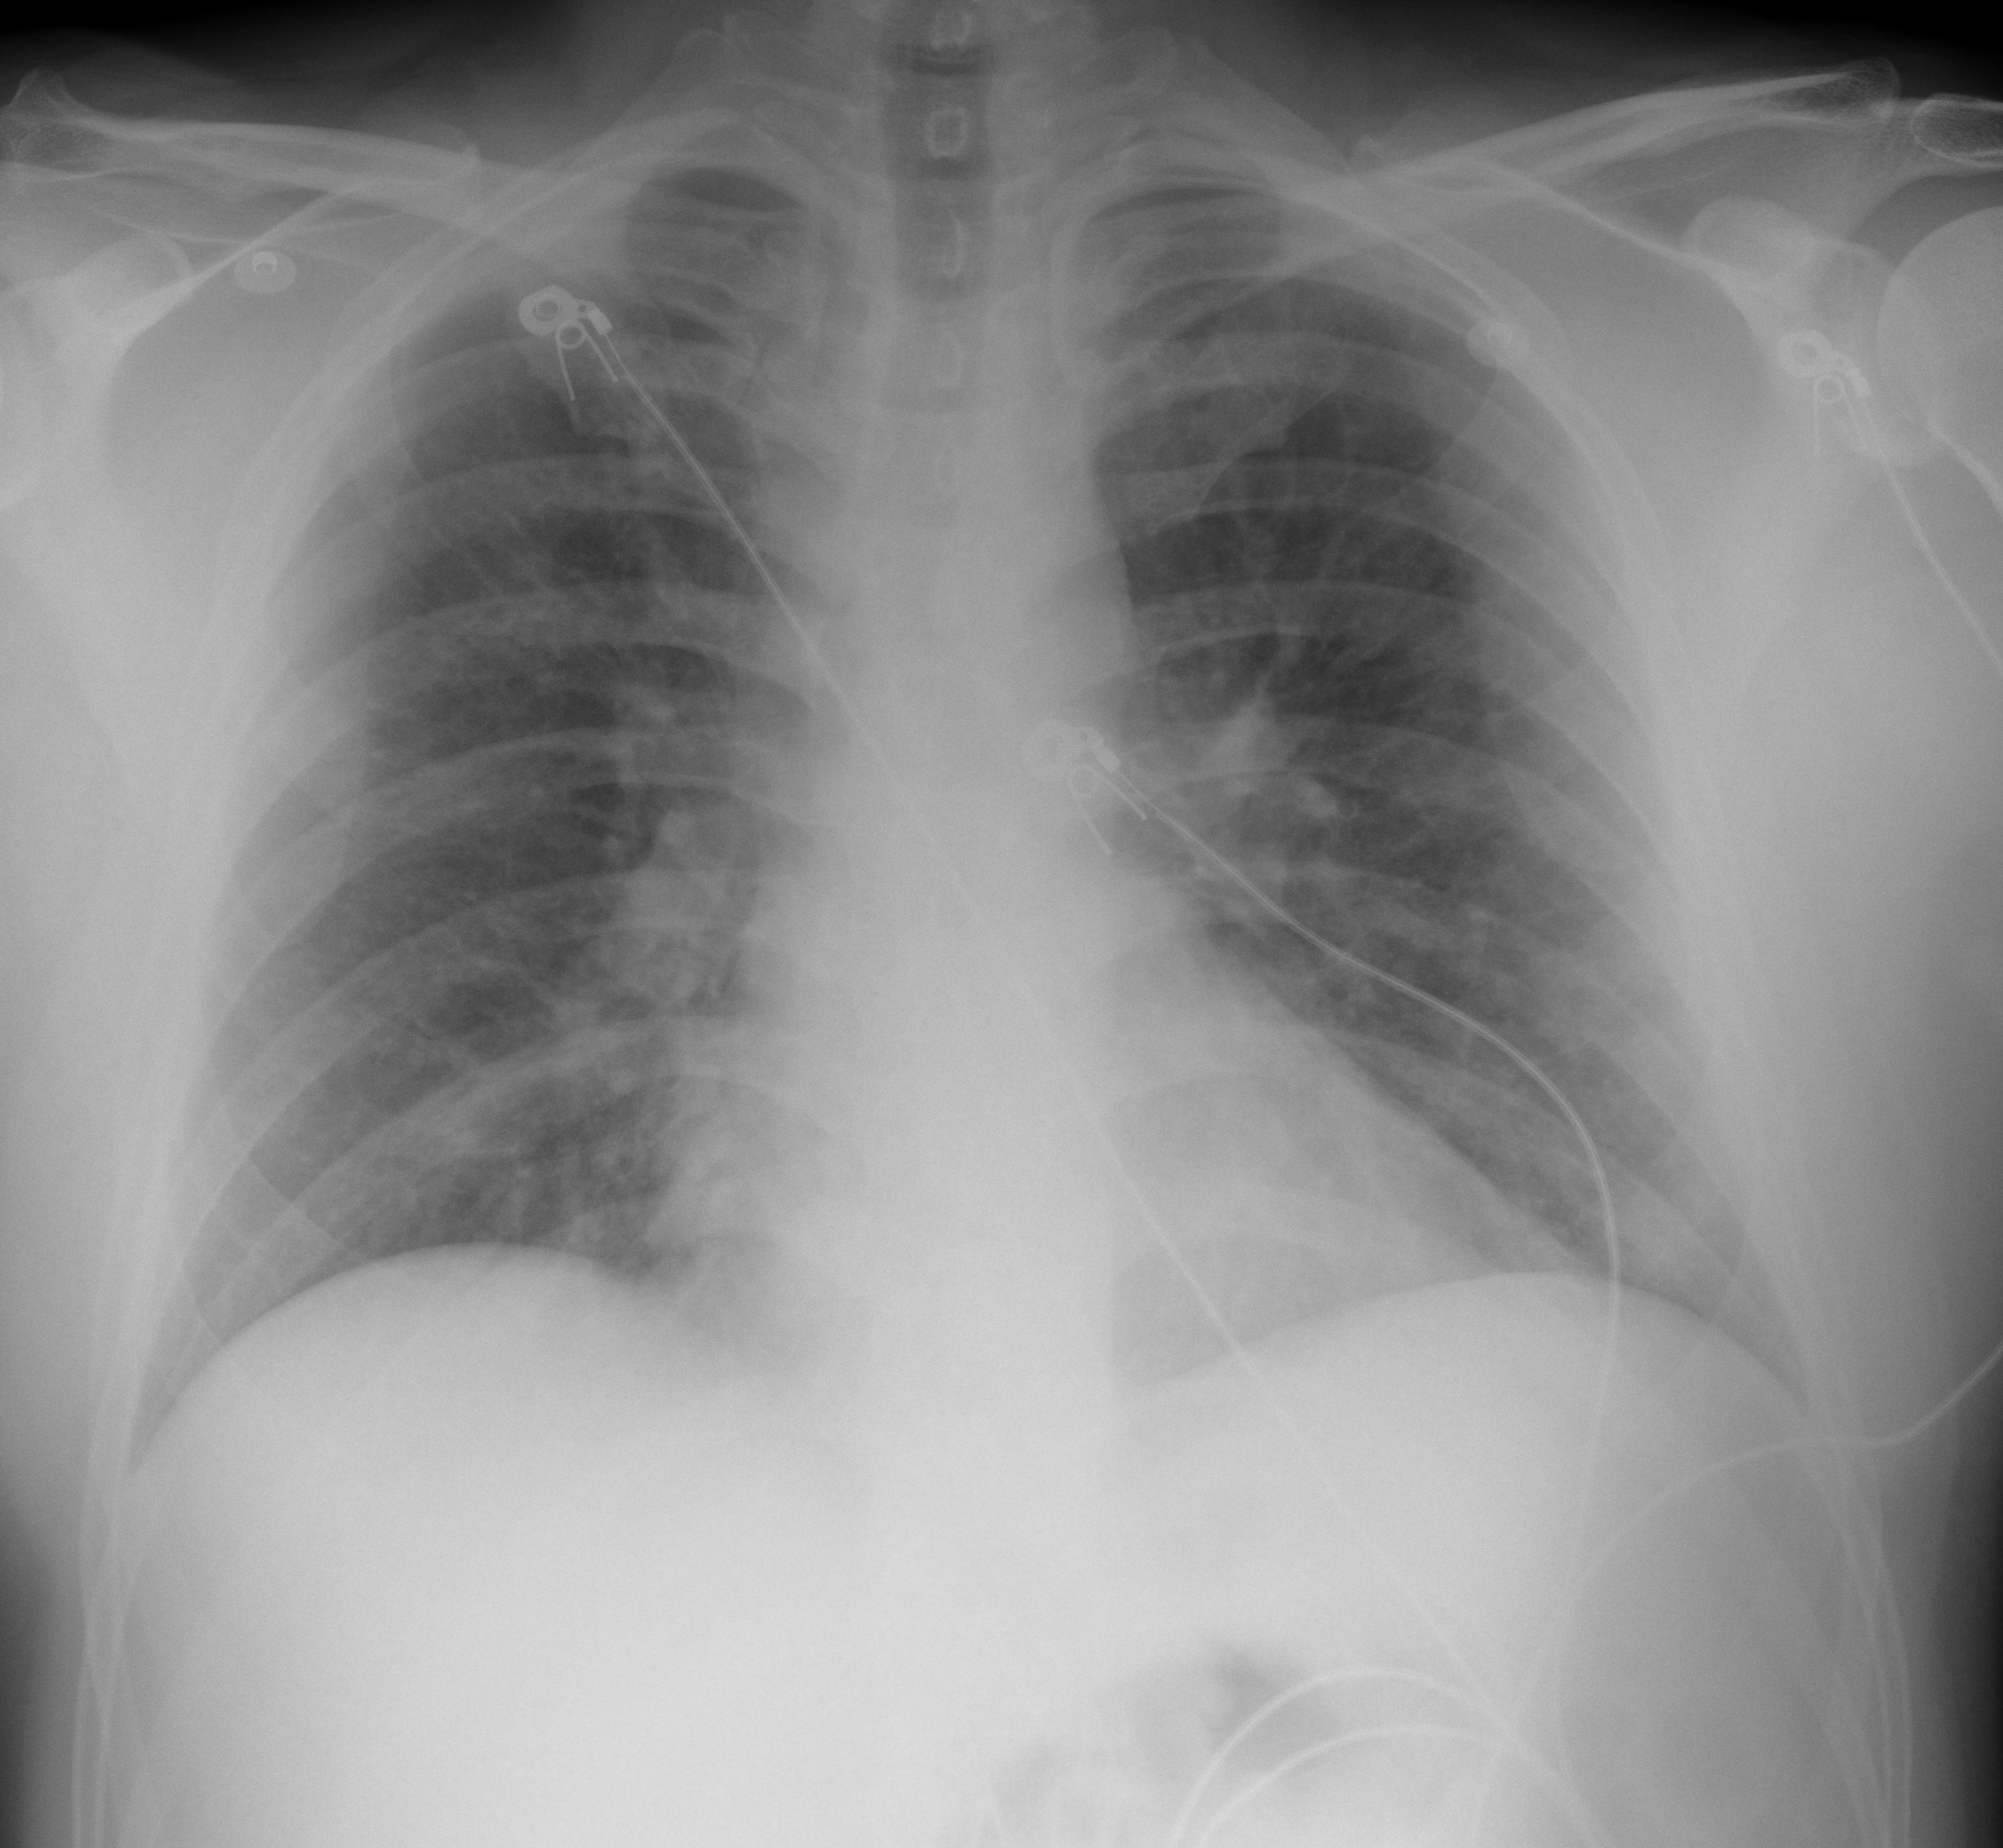
Portable chest radiograph, AP projection. Male patient, age 41 years; imaged 0 days after the COVID-19 diagnosis.
Radiologist key findings (as recorded): Hypoinflated lungs with bibasilar opacities.